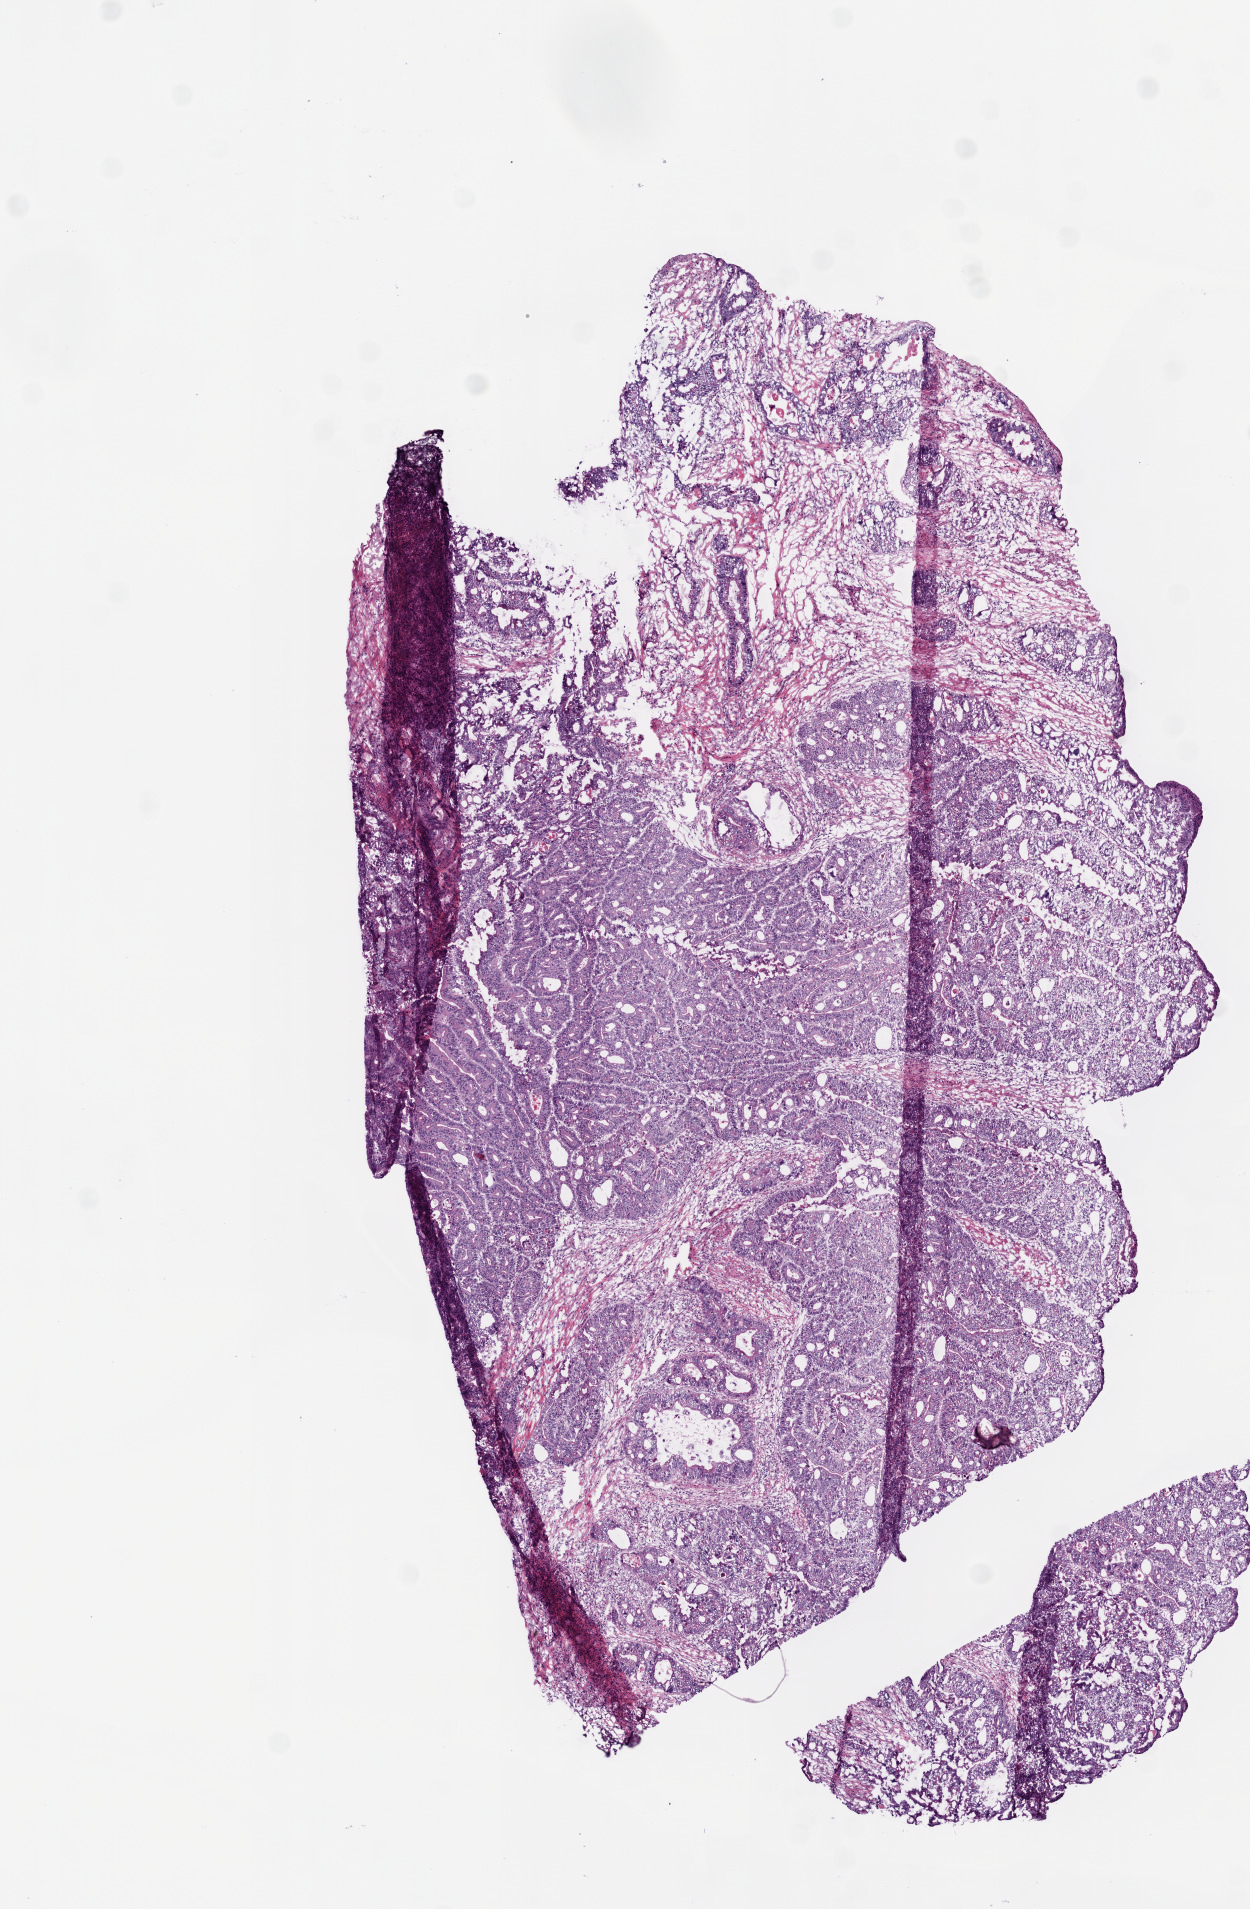
Digitized Hematoxylin and eosin (H&E) stained tissue section (whole slide) — whole scanned area (about 5.0 x 7.7 mm, acquisition: 20x scan) shown as a low-resolution overview. Frozen section from the bottom of the tissue portion. Colon, primary tumour sample. Female patient; age at initial diagnosis 84 years. Pathologist review of this section (percent, as recorded): tumour cells 85%, tumour nuclei 80%, normal cells 0%, stromal cells 10%, necrosis 5%.
• AJCC pathologic stage: IVA (7th edition)
• diagnosis: Adenocarcinoma, NOS
• lymph nodes positive (case pathology): 3 of 41 examined